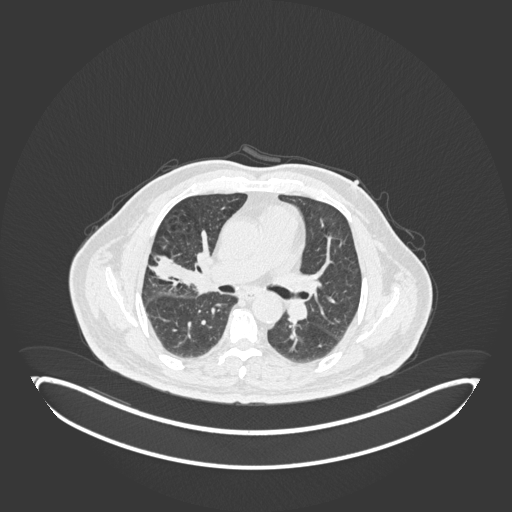
Chest CT, one axial slice; position 95 of 247 along the scan axis; 120 kVp; lung window (W 1500 / L -600 HU); 1 mm slice thickness; 512 × 512 image matrix, field of view 500 × 500 mm. Male patient, age 72 years. Case-level facts recorded for this patient, not image findings: clinical TNM (as recorded): T1c N0 M0; histopathological grade: G2.
Outlined on this slice (bounding box drawn by a radiologist):
- lung tumour (recorded histology: squamous cell carcinoma): bounding box <180,246,215,298> (left, top, right, bottom; pixels)